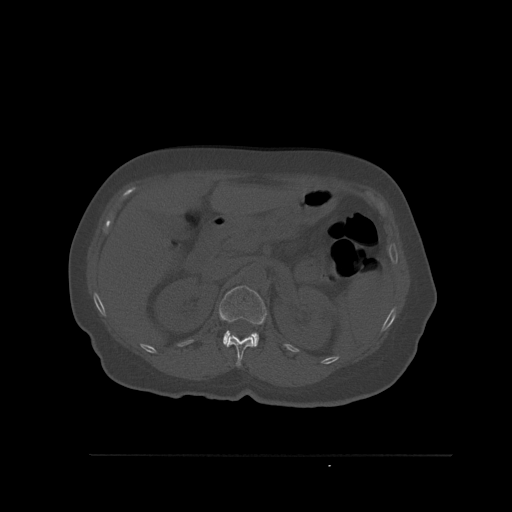
CT including the spine, one axial slice; slice 276 of 527 in the series (ordered by position); bone window (W 1800 / L 400 HU); 1.5 mm slice thickness; 512 × 512 image matrix. Female patient, age 73 years. Case-level facts recorded for this patient, not image findings: primary cancer: breast; vertebrae with lytic lesions (as recorded): L2.
Structures marked on this image (semi-automatically segmented with operator editing):
- L1 vertebra: box from (x=218, y=285) to (x=267, y=347) px
- T12 vertebra: (x=227, y=333)–(x=254, y=367)